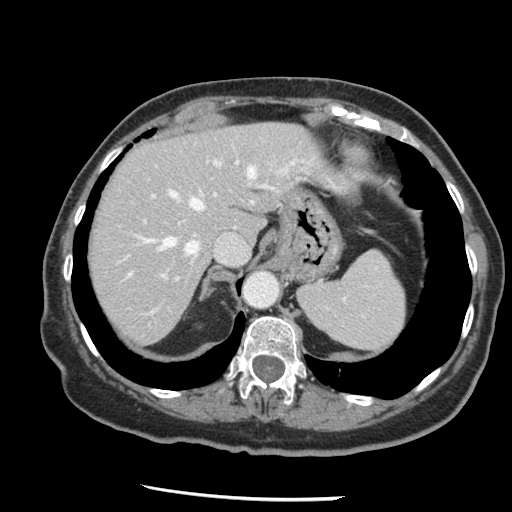
Contrast-enhanced abdominal CT, one axial slice. Slice 104 of 148 in the series (ordered by position). Intravenous contrast given. Soft-tissue window (W 400 / L 40 HU). 512 × 512 image matrix, field of view 330 × 330 mm. Female patient, age 85 years. From the clinical record (not read from this slice): diagnosis: colorectal cancer liver metastases, imaged before liver resection; multiple liver metastases: no; largest metastasis: 0.9 cm.
Outlined on this slice (manually delineated by an expert):
- hepatic veins: bounding box (x1, y1, x2, y2) in pixels: (129, 138, 290, 275)
- liver: (89, 123, 328, 344)
- planned liver remnant (the part of the liver to remain after resection): (89, 123, 328, 344)
- portal vein (with intrahepatic branches): (144, 157, 274, 281)